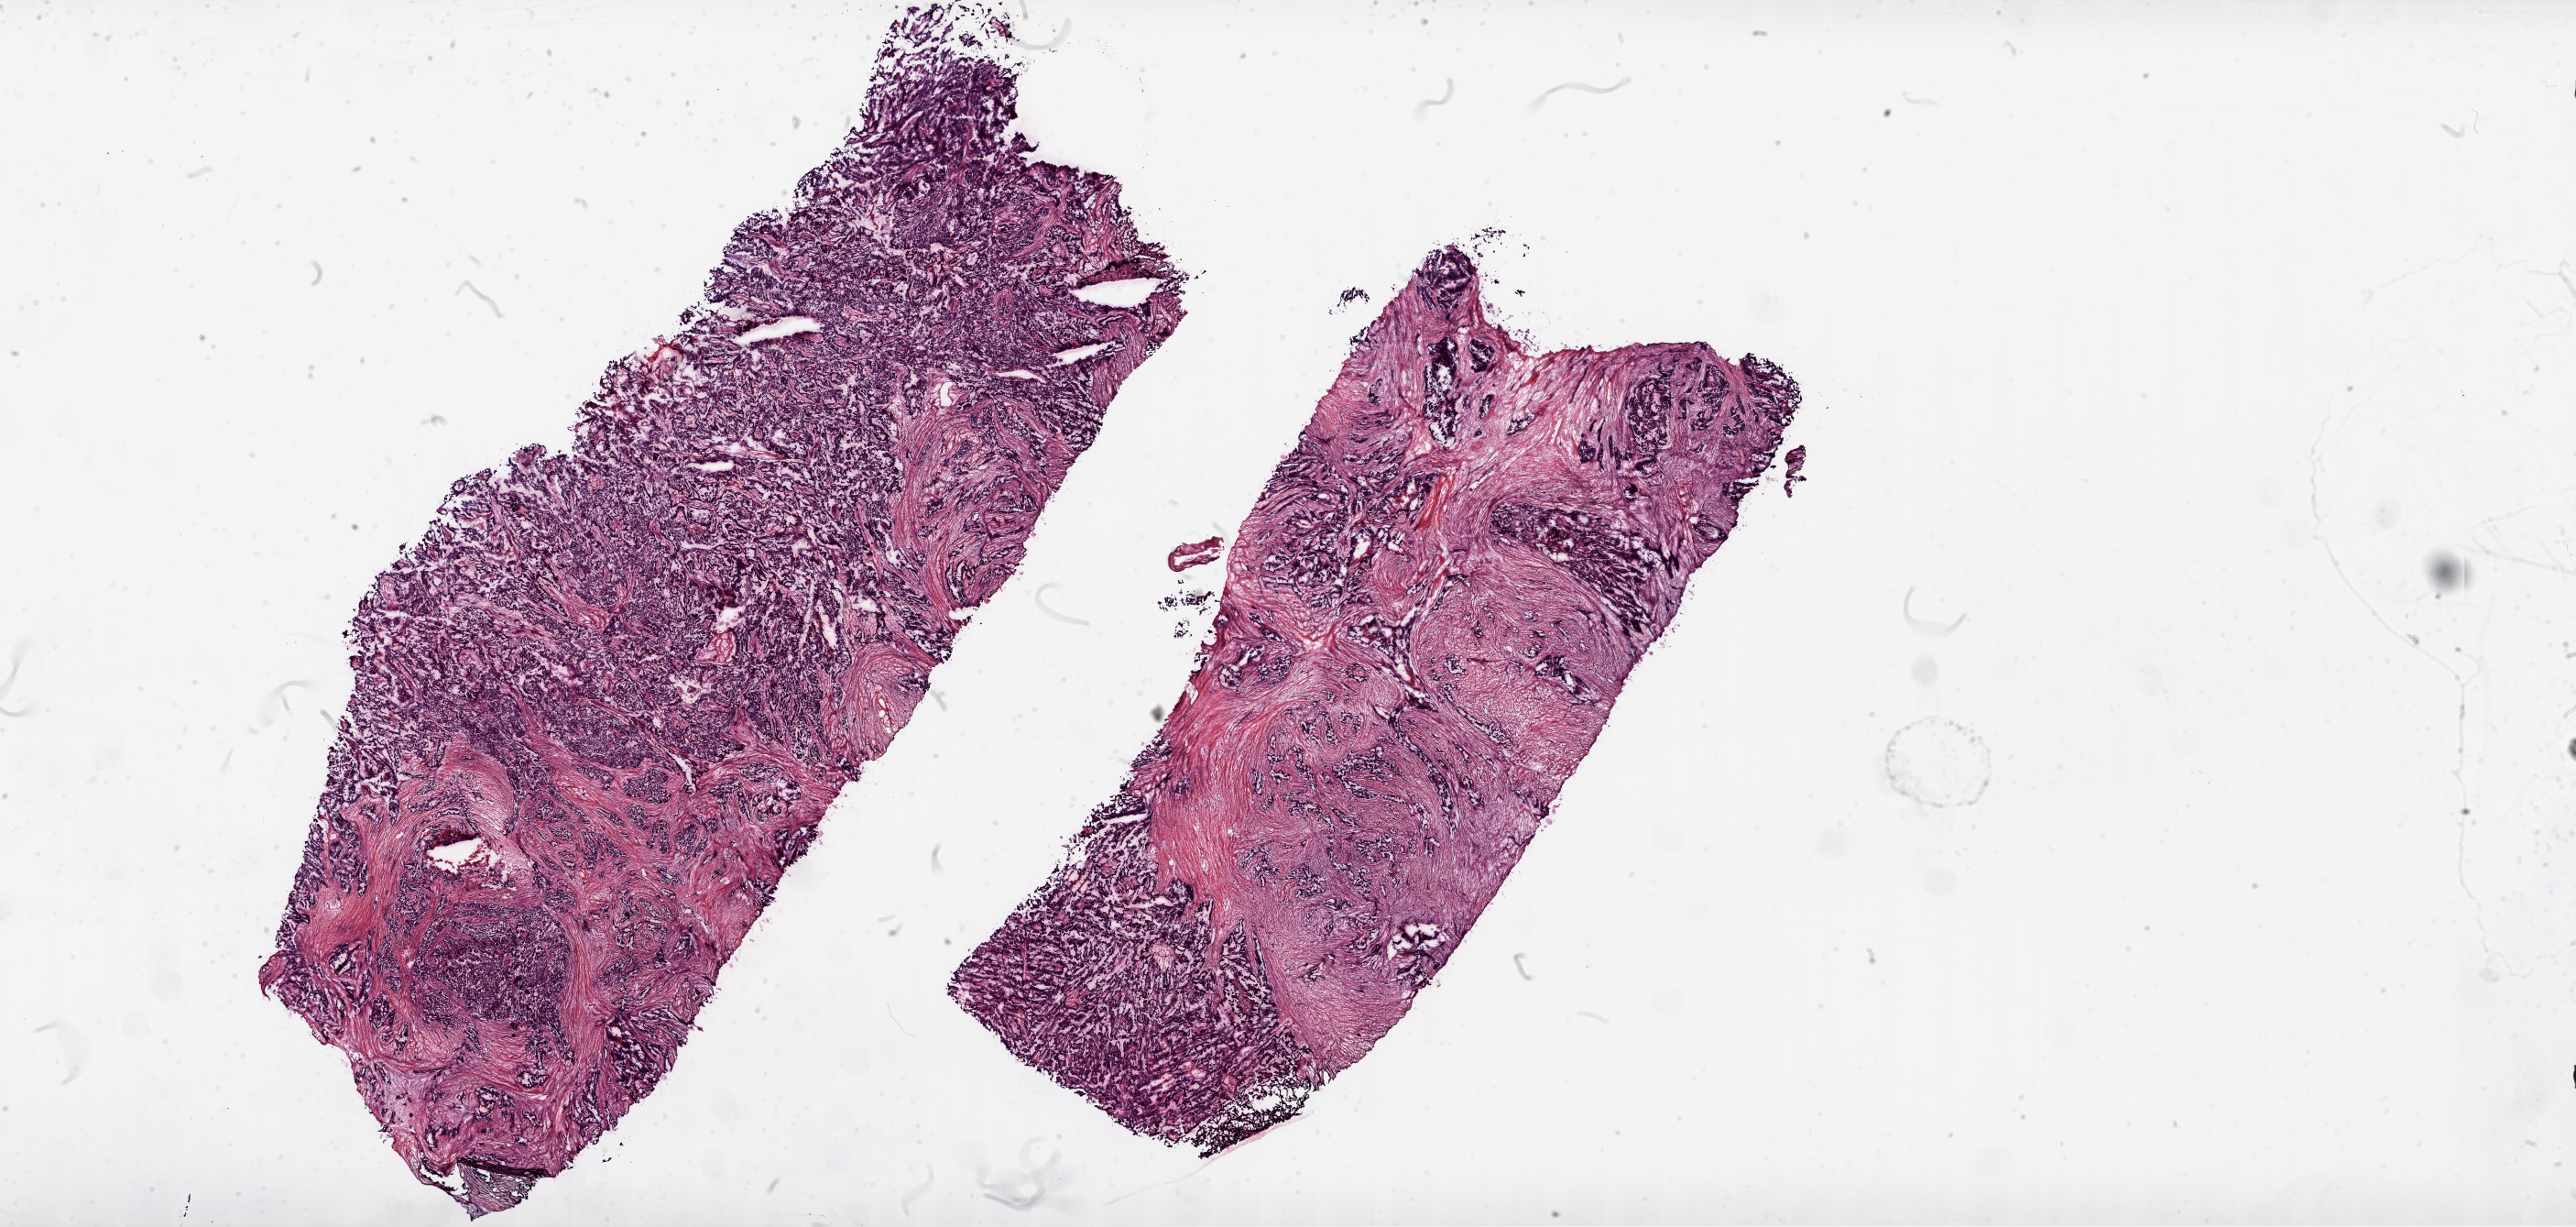
Digitized Hematoxylin and eosin (H&E) stained tissue section (whole slide), whole scanned area (about 45.1 x 21.5 mm) shown as a low-resolution overview; frozen section from the top of the tissue portion; primary tumour sample from the ovary. Female, age 60 years at initial diagnosis. Histologic grade: G2 (moderately differentiated). Slide review estimates, as recorded: tumour cells 79%, tumour nuclei 80%, normal cells 0%, stromal cells 20%, necrosis 1%.
Diagnosis: Serous cystadenocarcinoma, NOS. Laterality: bilateral. FIGO stage: IIIC.